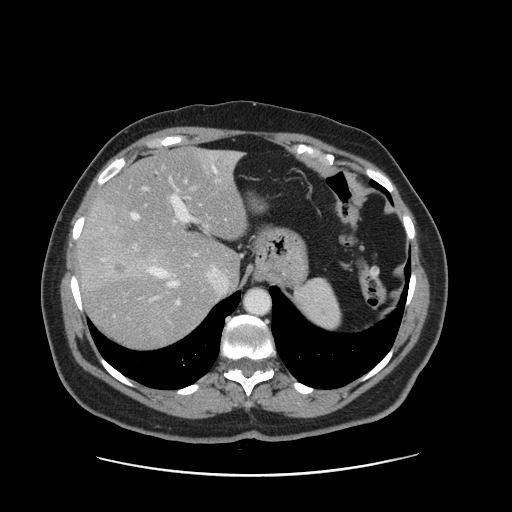
Contrast-enhanced abdominal CT, one axial slice; position 113 of 161 along the scan axis; 120 kVp; soft-tissue window (W 400 / L 40 HU); 2.5 mm slice thickness; 512 × 512 image matrix. Female patient, age 62 years. Case-level facts recorded for this patient, not image findings: diagnosis: colorectal cancer liver metastases, imaged before liver resection; multiple liver metastases: no; largest metastasis: 2.5 cm.
Structures marked on this image (outlined manually by an expert reader):
- hepatic veins: bounding box [x1, y1, x2, y2] px = [132, 168, 227, 290]
- liver: [80, 149, 247, 350]
- planned liver remnant (the part of the liver to remain after resection): [97, 148, 247, 282]
- portal vein (with intrahepatic branches): [114, 176, 197, 317]
- liver metastasis: [116, 264, 124, 274]